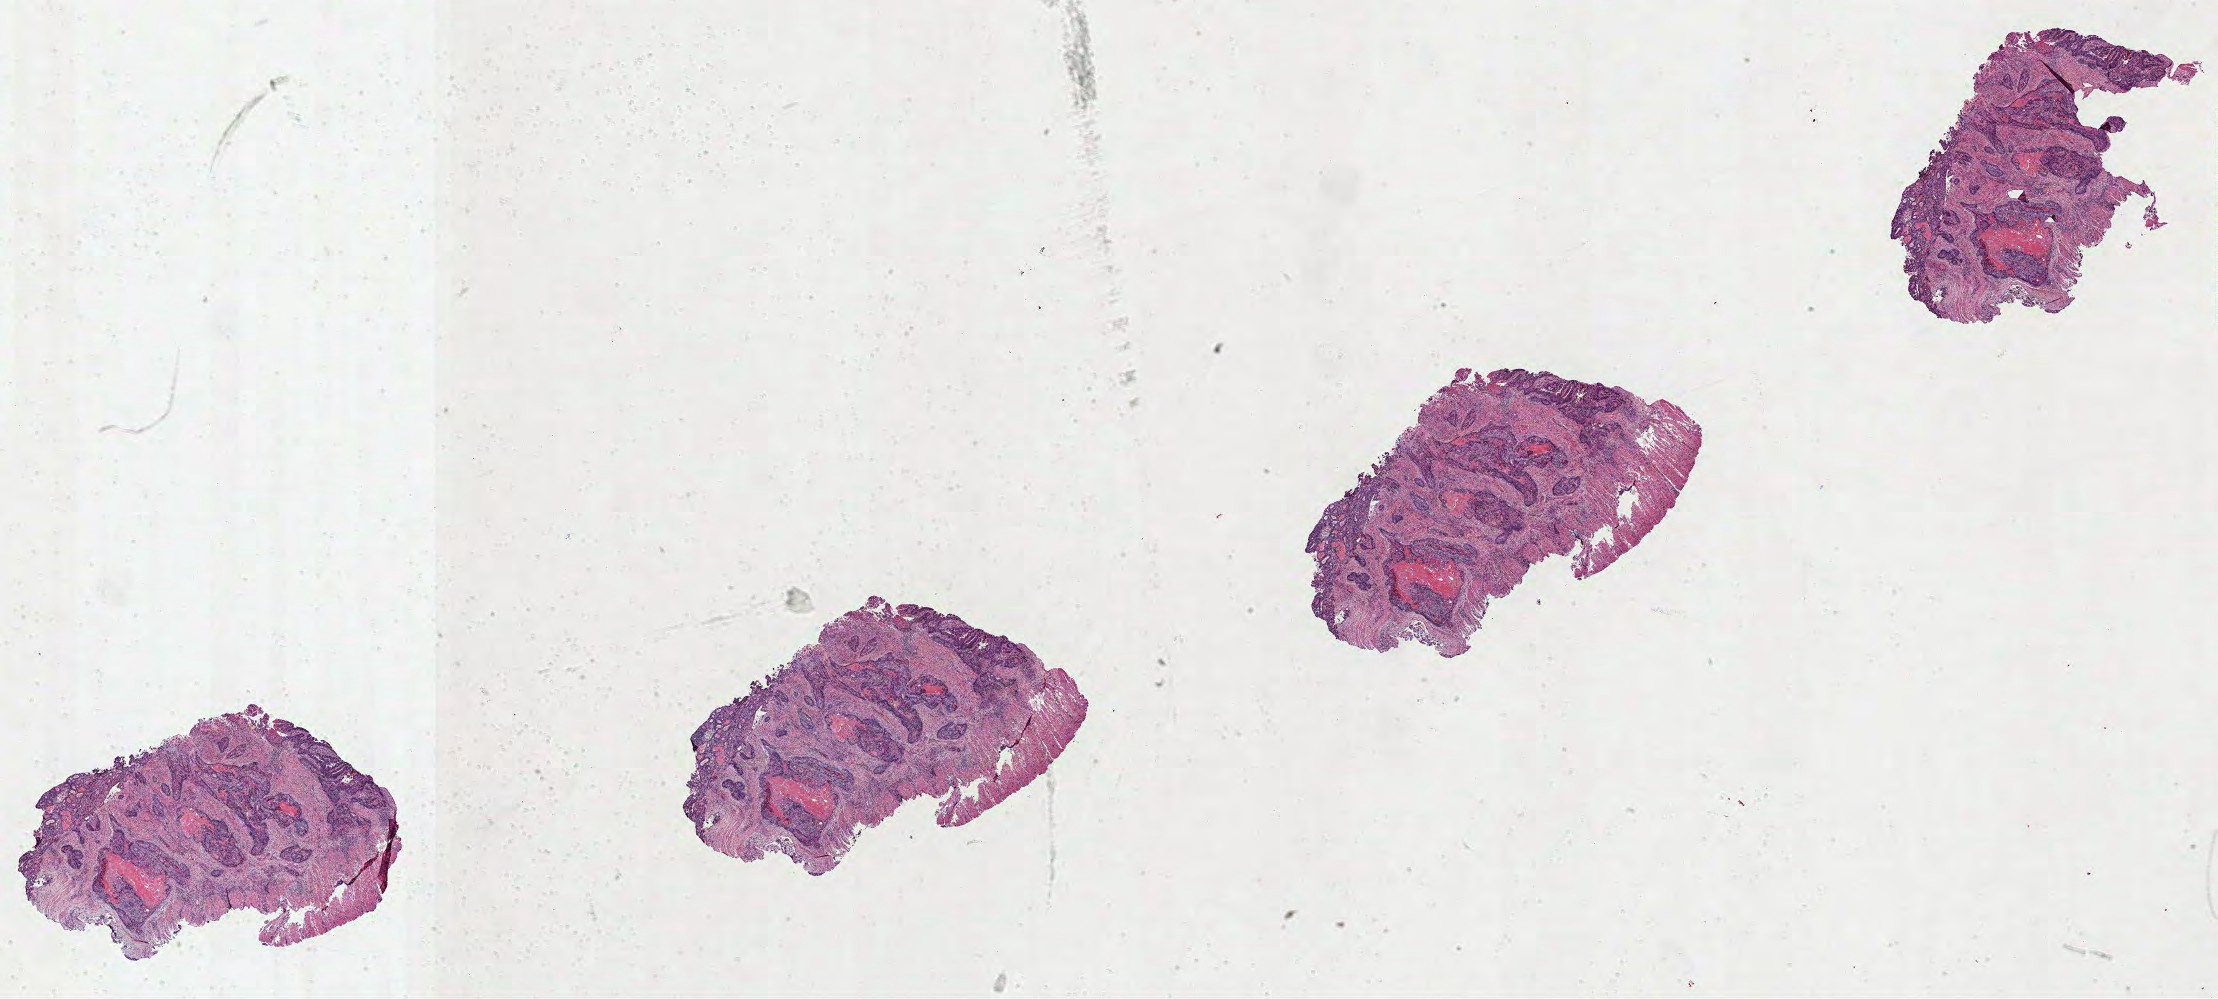
Digitized Hematoxylin and eosin (H&E) stained tissue section (whole slide), shown as a low-resolution overview of the whole scanned area (about 35.8 x 16.1 mm). Formalin-fixed paraffin-embedded (FFPE) diagnostic section. Sample: primary tumour, colon. Female patient; age at initial diagnosis 55 years.
Lymph nodes positive (case pathology): 2 of 33 examined. TNM: T3 N1b MX. Diagnosis: Adenocarcinoma, NOS. AJCC pathologic stage: IIIB.